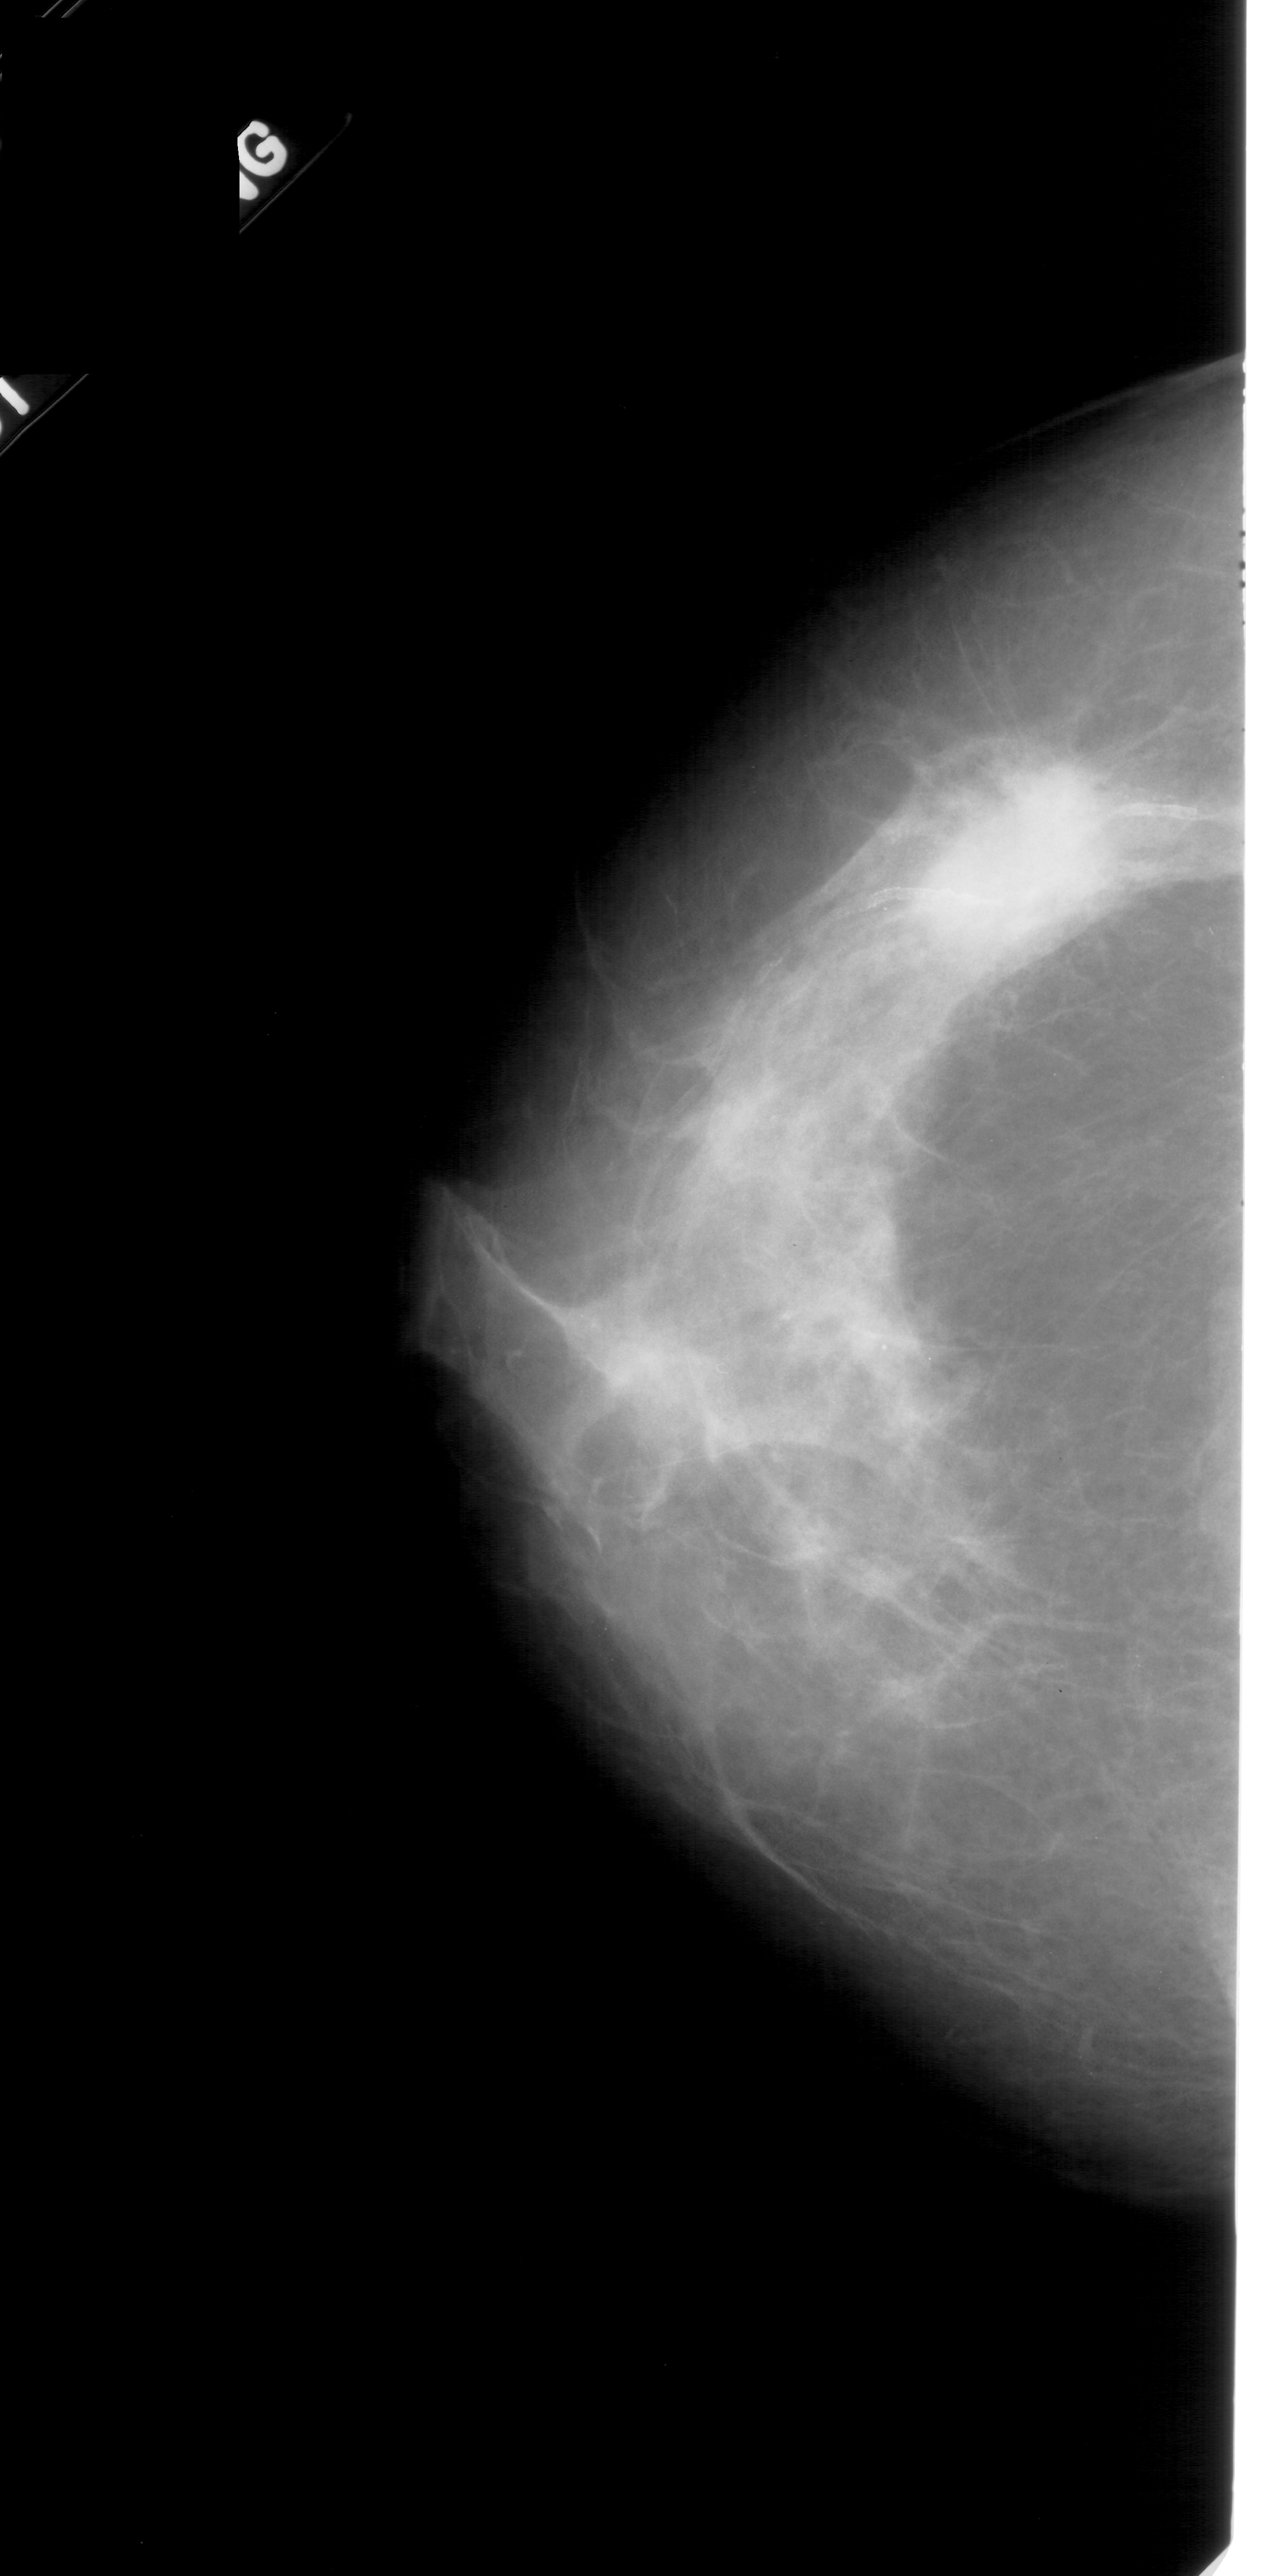
Digitized screen-film mammogram. Left breast. Craniocaudal (CC) view. BI-RADS breast density category 2 (scale 1–4). 1284 × 2576 image matrix.
Marked abnormalities (boxes around the expert regions of interest):
- mass, shape oval, margins ill defined; BI-RADS assessment category 4; subtlety rating 4 on a 1 (subtle) to 5 (obvious) scale; pathology result (as recorded, not read from the image): malignant: bounding box [x1, y1, x2, y2] px = [959, 772, 1111, 931]